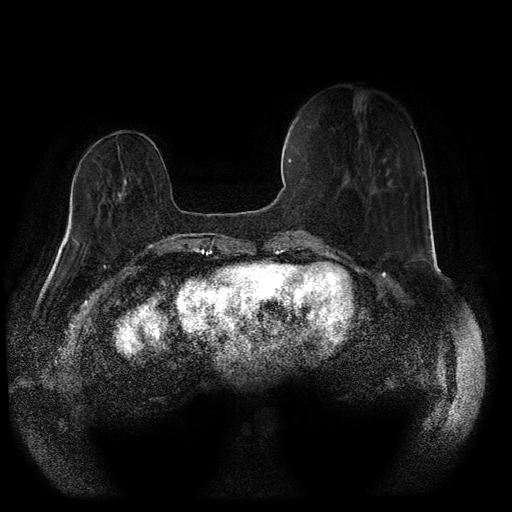
Breast MRI (dynamic contrast-enhanced, multi-phase), one axial slice. Slice 21 of 116 in the series (ordered by position). Dynamic contrast-enhanced series, time point 2 of 5 at this slice position (early post-contrast). 1.5 T. TE 2.6 ms, TR 5.3 ms. 2 mm slice thickness. 512 × 512 image matrix, field of view 360 × 360 mm. Patient: female, 71 years.
Structures marked on this image (semi-automatic segmentation, software-assisted and operator-edited):
- breast lesion (labelled 'tumour' in the annotation; benign lesions carry a separate 'benign' label): bounding box <117,180,127,200> (left, top, right, bottom; pixels)